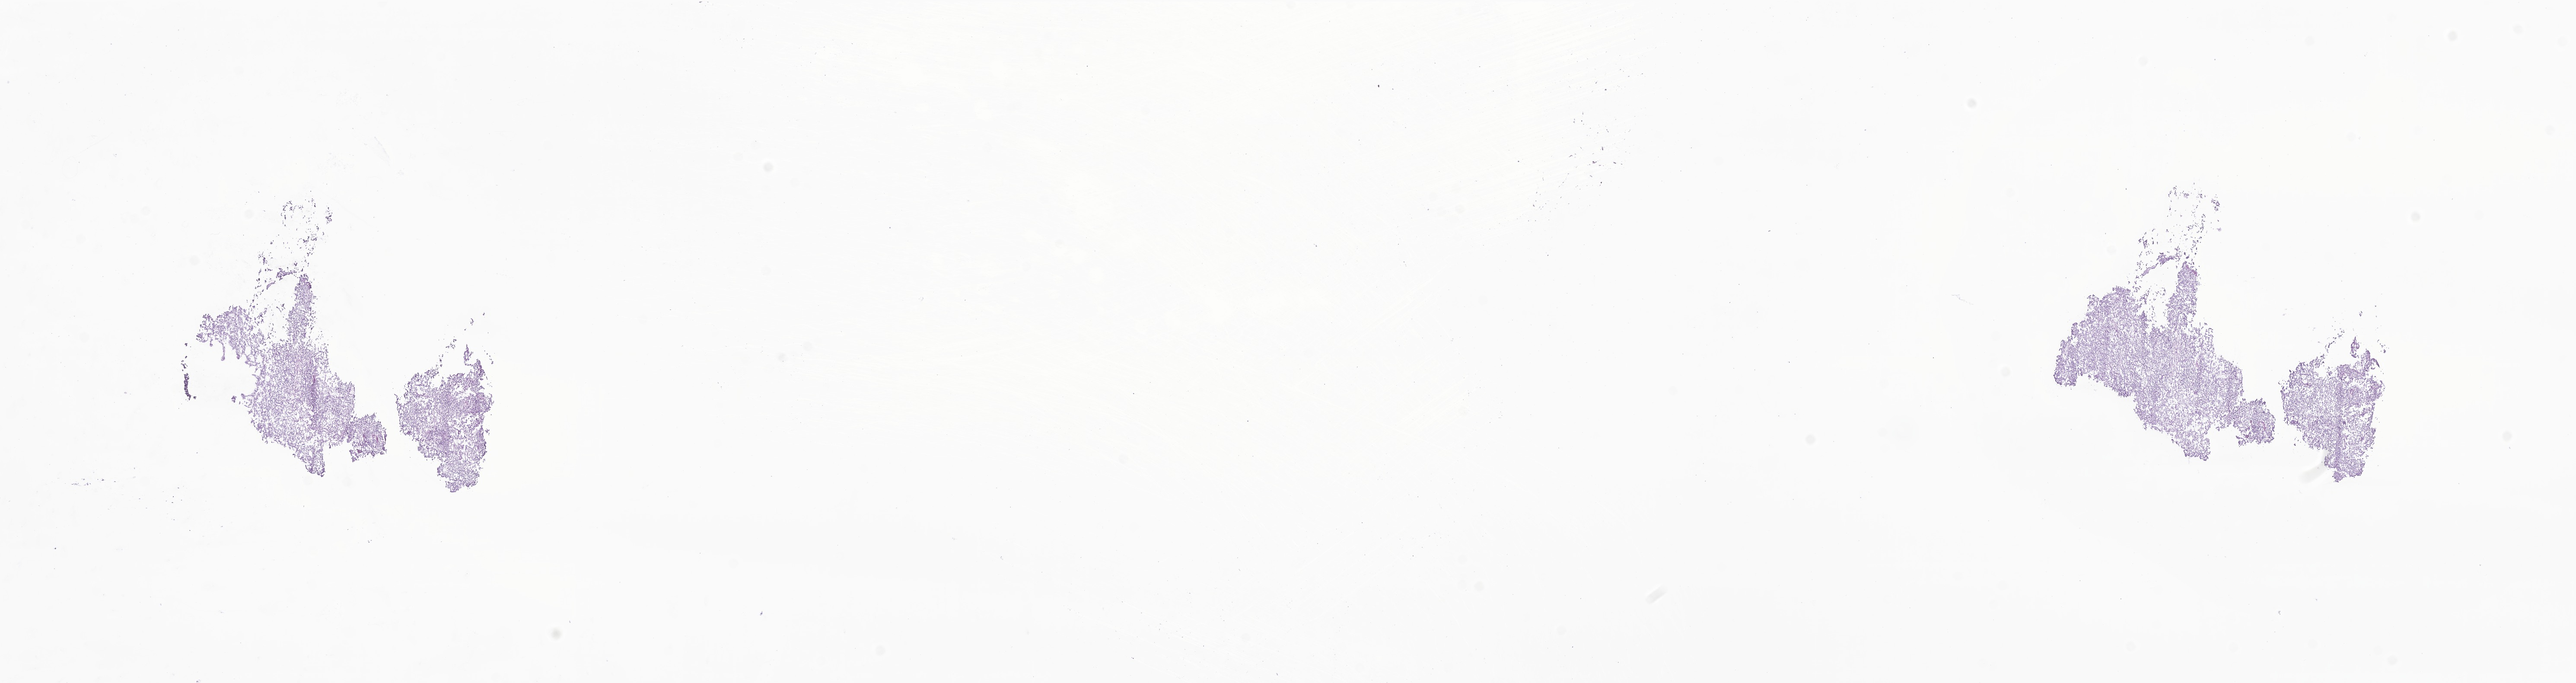
Whole-slide image, H&E stain of tumor tissue from the brain — a low-resolution overview of the entire scanned area, about 25.1 x 6.7 mm; cryosection (OCT / tissue freezing medium). Male patient, age 677 days (about 1.9 years).
Diagnosis (ICD-O-3 morphology term): Atypical teratoid/rhabdoid tumor.